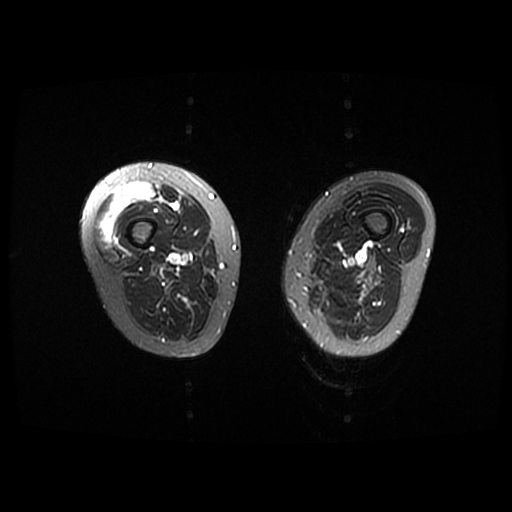
MRI of an extremity soft-tissue mass, one axial slice. Position 5 of 42 along the scan axis. T2-weighted fat-saturated. 6 mm slice thickness. 512 × 512 image matrix, field of view 440 × 440 mm. Female patient. From the clinical record (not read from this slice): histological type: pleiomorphic undifferentiated sarcoma; grade: high; site of the primary tumour: right quadricep.
Annotated regions visible in this slice (outlined manually by an expert reader):
- gross tumour volume including surrounding oedema: bounding box [x1, y1, x2, y2] px = [97, 183, 155, 242]